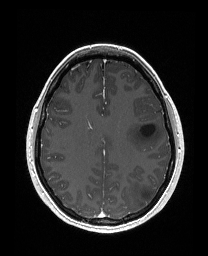
Brain MRI from a brain-tumour surgery series, one axial slice. Slice 105 of 176 in the series (ordered by position). T1-weighted post-contrast. 1 mm slice thickness. 208 × 256 image matrix, field of view 203 × 250 mm. Case-level facts recorded for this patient, not image findings: histopathology: Astrocytoma; WHO grade: 3; IDH mutation: yes.
Outlined on this slice (outlined manually by an expert reader):
- tumour: bounding box [x1, y1, x2, y2] px = [125, 120, 161, 150]